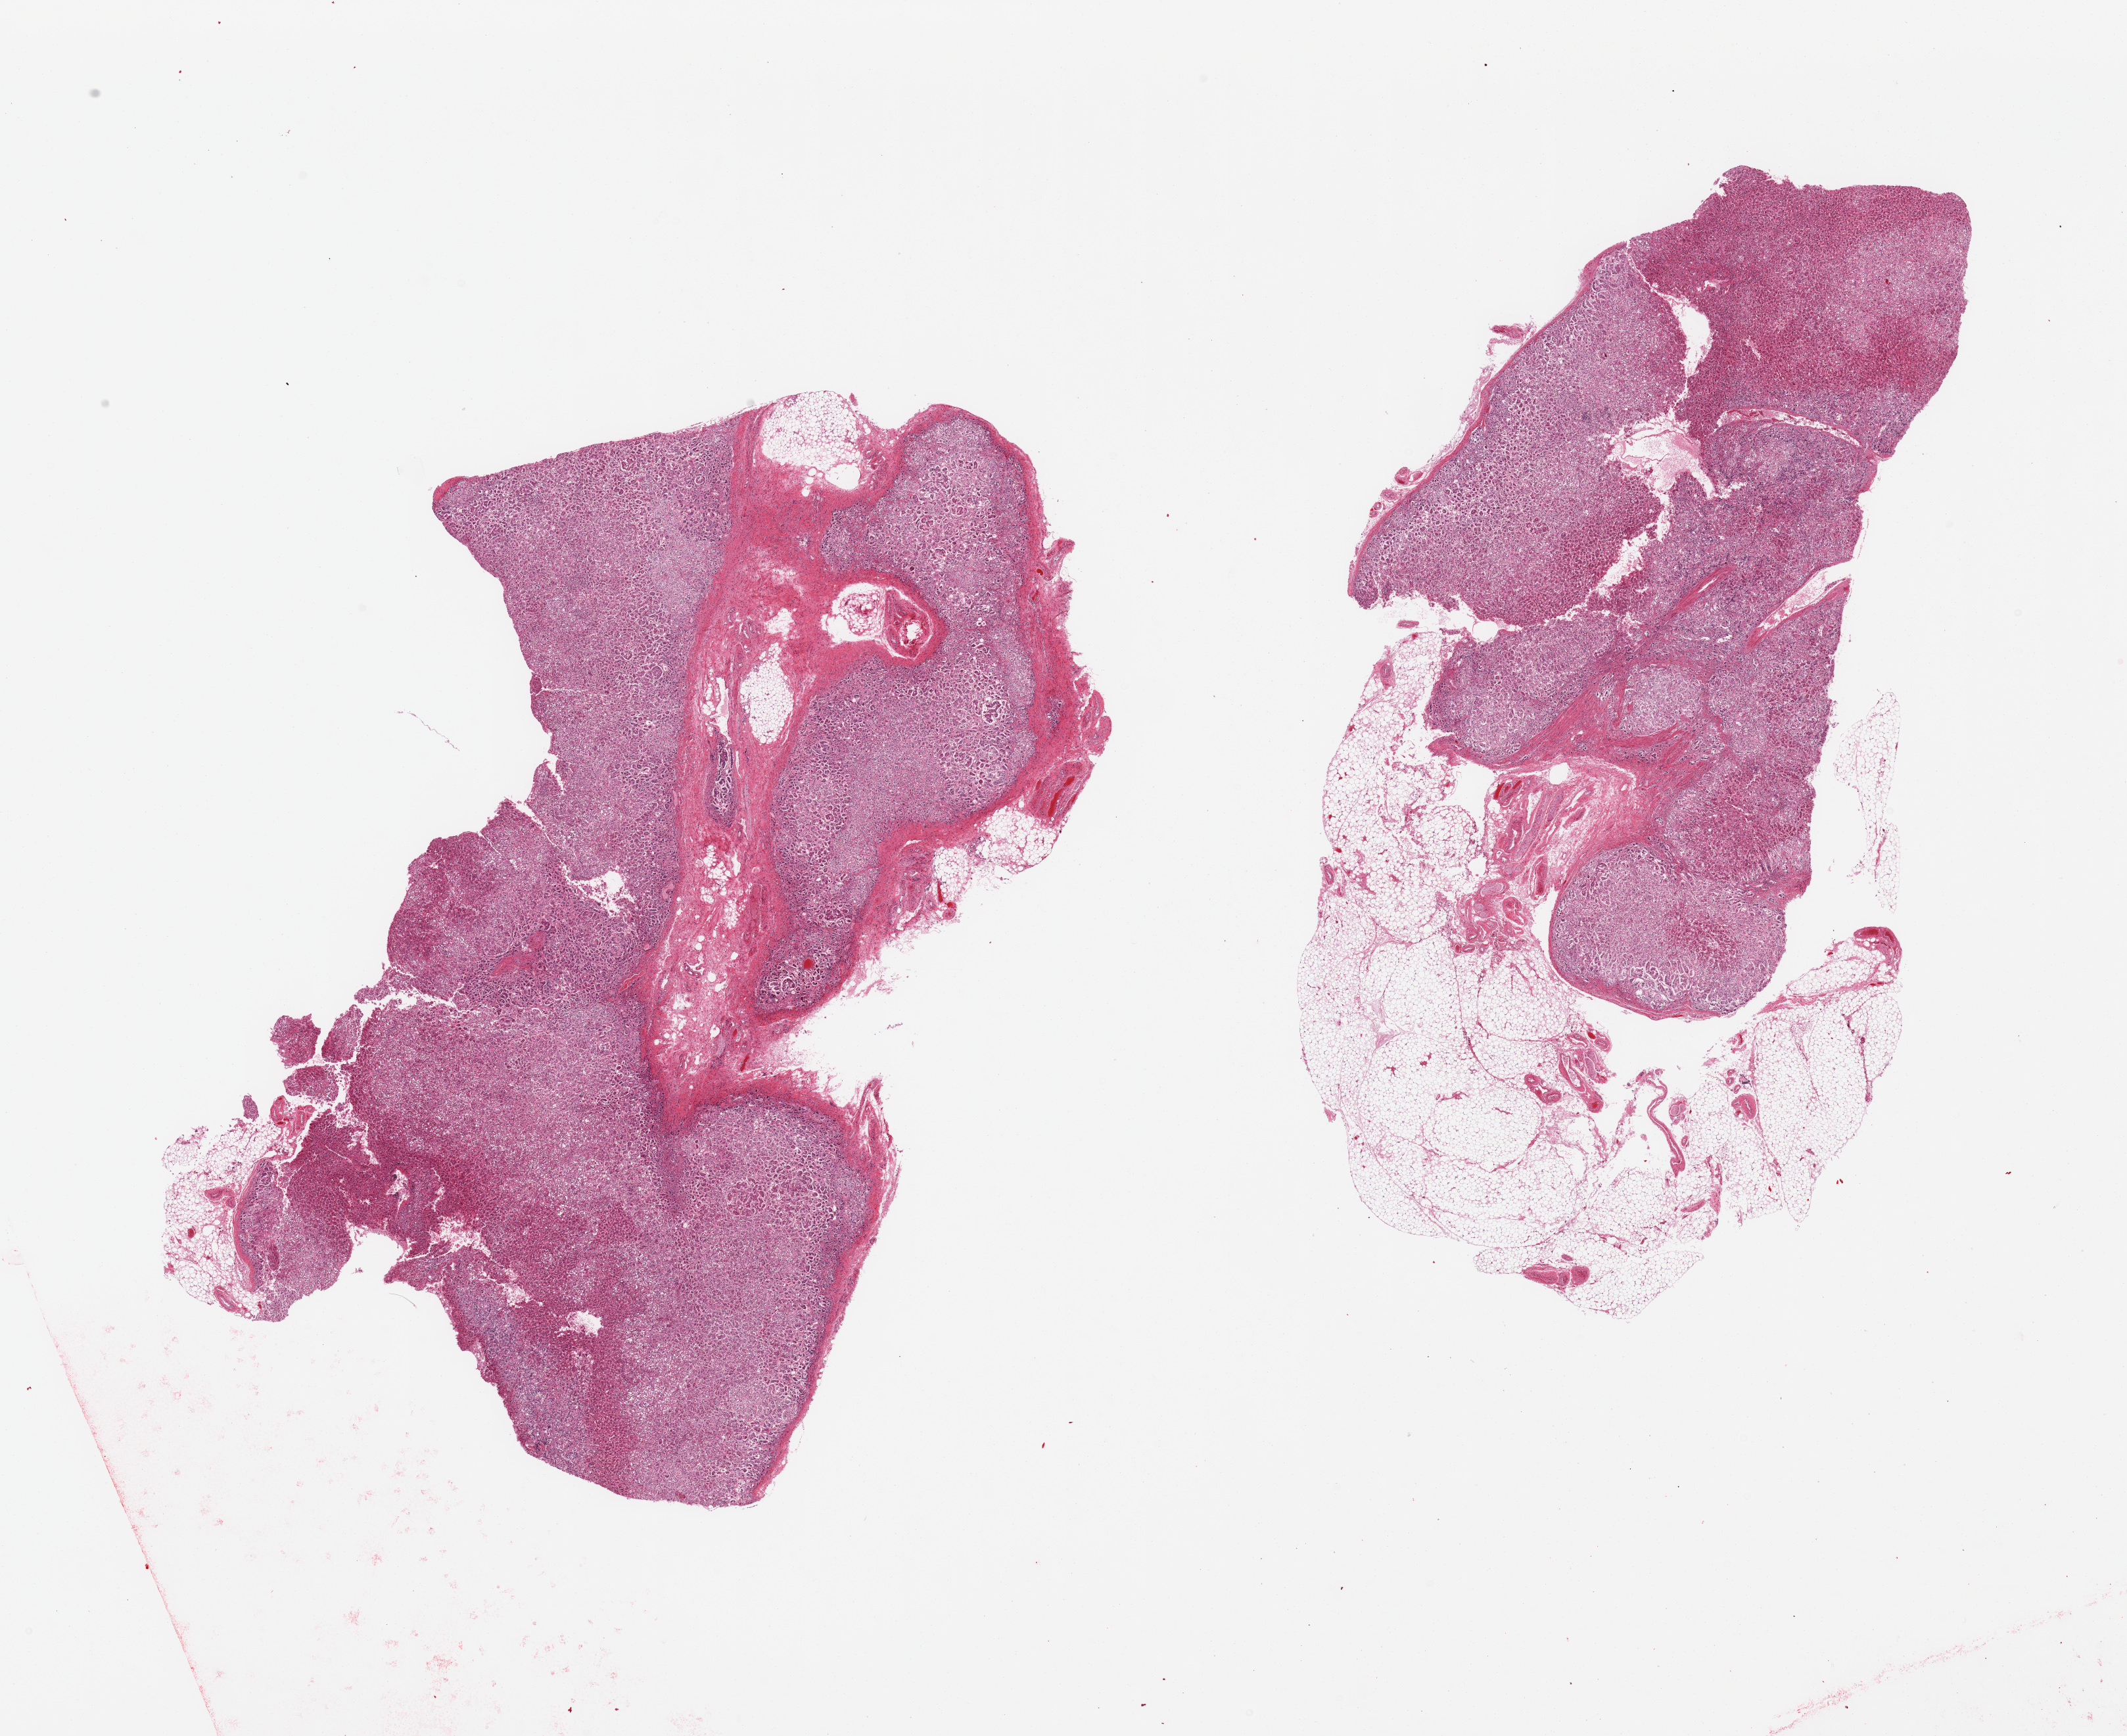
H&E whole-slide image, brightfield, a low-resolution overview of the entire scanned area, about 25.6 x 20.9 mm, PAXgene-fixed paraffin-embedded (PFPE) section, section of adrenal gland (target tissue), tissue donor sample. Female donor.
Reviewer comment on this tissue sample: 2 pieces, cortex, ~30% adherent/interstitial fat/fibrous tissue.